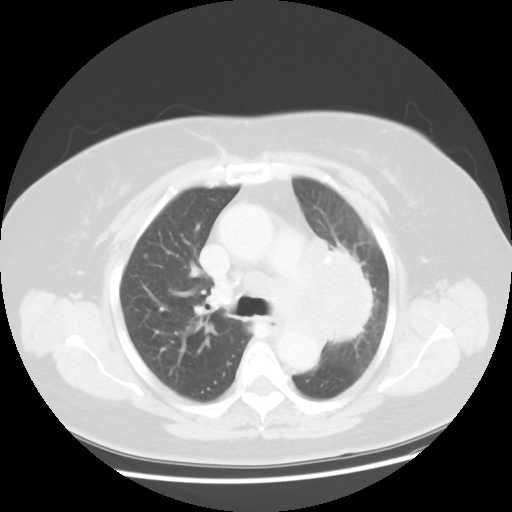
Chest CT, one axial slice. Position 31 of 49 along the scan axis. Reconstruction kernel STANDARD. Lung window (W 1500 / L -600 HU). 5 mm slice thickness. 512 × 512 image matrix, field of view 374 × 374 mm. Patient: female, 58 years. Case-level facts recorded for this patient, not image findings: clinical TNM (as recorded): T4 N3 M0; histopathological grade: G3.
Outlined on this slice (bounding box drawn by a radiologist):
- lung tumour (recorded histology: small cell carcinoma): bounding box (x1, y1, x2, y2) in pixels: (252, 218, 372, 345)